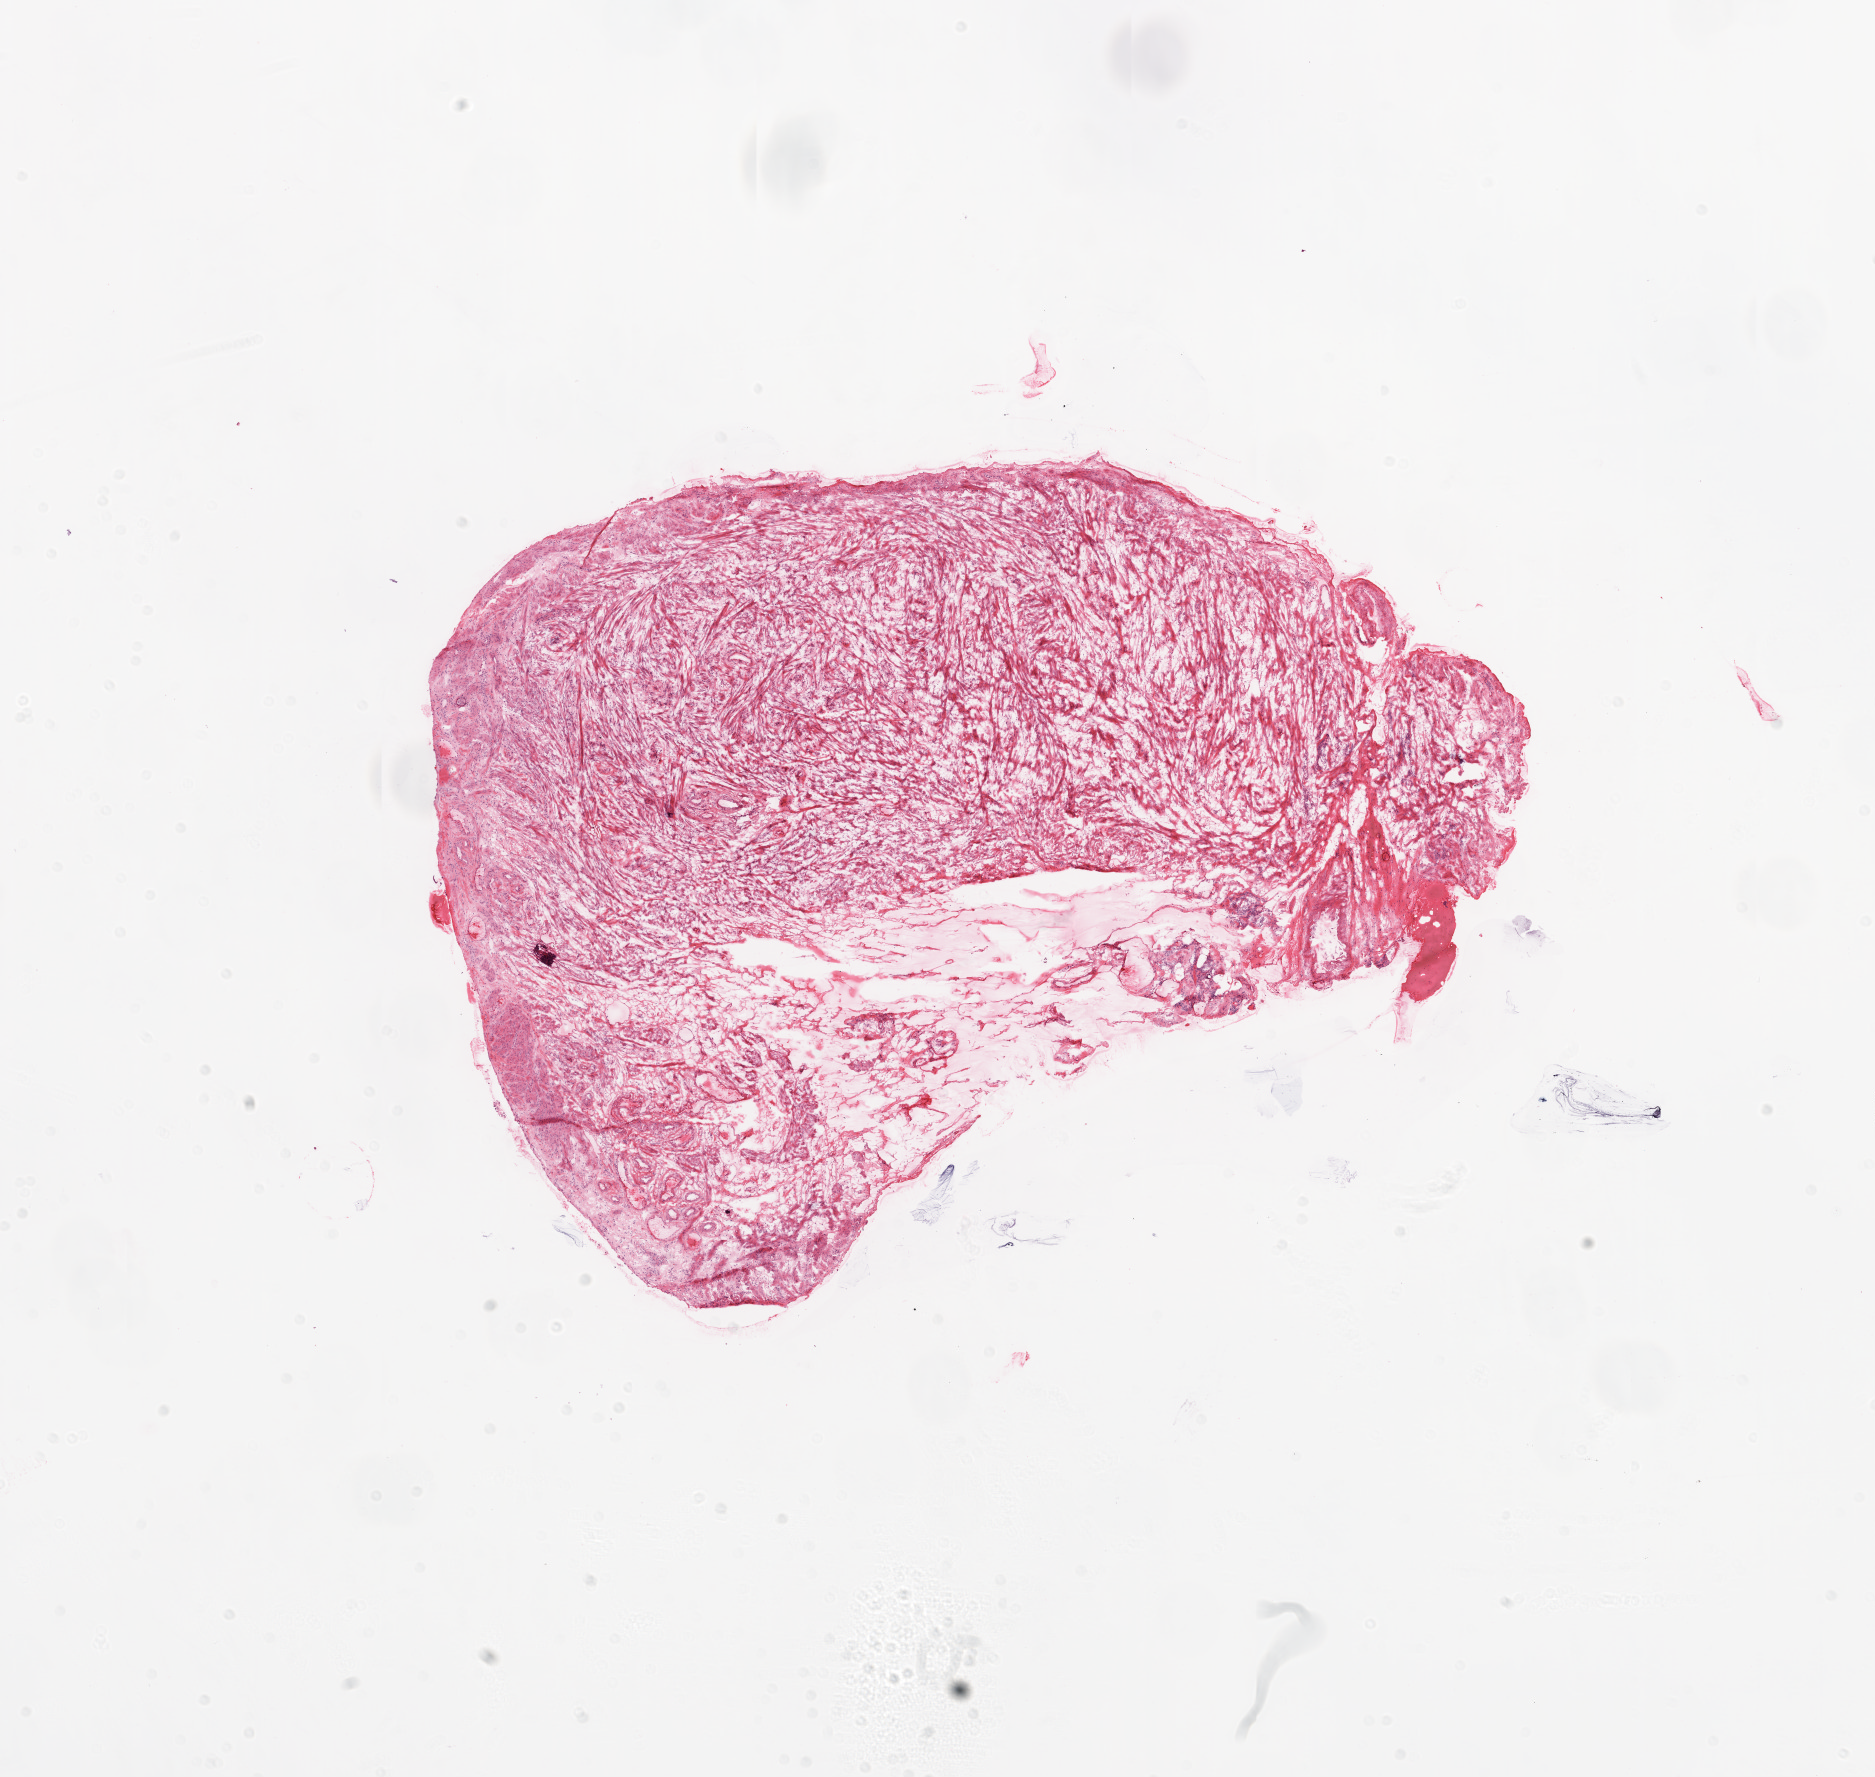
Whole-slide histology image, H&E, shown as a low-resolution overview of the whole scanned area (about 15.0 x 14.3 mm, from a 20x scan); frozen section from the top of the tissue portion; solid tissue normal (non-tumour tissue) sample from the ovary. Female, age 51 years at initial diagnosis.
This section: solid tissue normal sample (biorepository sample class). Patient diagnosis: Serous cystadenocarcinoma, NOS.